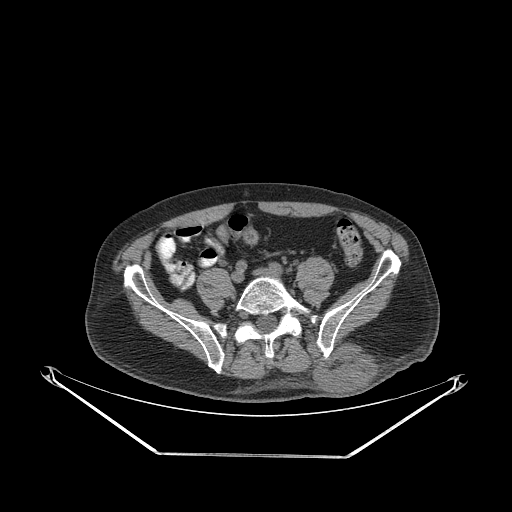
CT of an extremity soft-tissue mass (from a PET/CT study), one axial slice; position 85 of 267 along the scan axis; 140 kVp; soft-tissue window (W 400 / L 40 HU); 3.75 mm slice thickness; 512 × 512 image matrix. Male patient. From the clinical record (not read from this slice): histological type: leiomyosarcoma; grade: intermediate; site of the primary tumour: left pelvis.
Outlined on this slice (expert contour drawn on MRI and transferred to this co-registered scan by the dataset authors):
- gross tumour volume (mass): box from (x=313, y=340) to (x=378, y=394) px